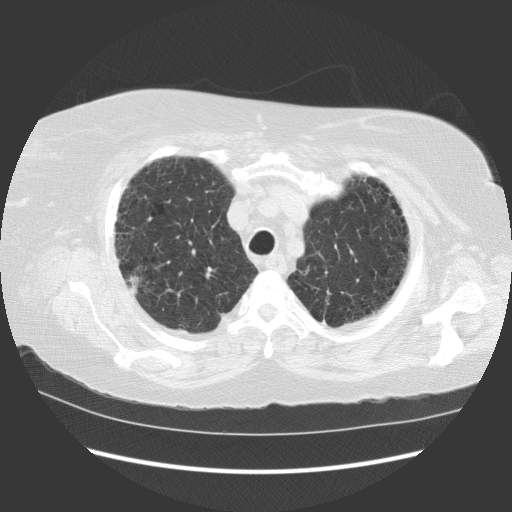
Low-dose screening chest CT, one axial slice. Position 98 of 121 along the scan axis. Reconstruction kernel STANDARD. 140 kVp. Lung window (W 1500 / L -600 HU). 512 × 512 image matrix, field of view 380 × 380 mm.
Outlined on this slice (outlined manually by an expert reader):
- lesion 1 (tumor, upper lobe of right lung): bounding box (x1, y1, x2, y2) in pixels: (129, 276, 139, 294)